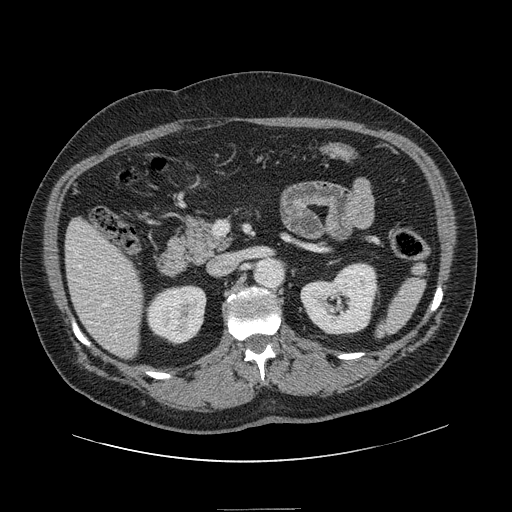
Contrast-enhanced abdominal CT, one axial slice. Position 60 of 154 along the scan axis. 120 kVp. Intravenous contrast given. Soft-tissue window (W 400 / L 40 HU). 2.5 mm slice thickness. 512 × 512 image matrix. Male patient, age 61 years. Case-level facts recorded for this patient, not image findings: diagnosis: colorectal cancer liver metastases, imaged before liver resection; multiple liver metastases: yes; largest metastasis: 2.6 cm; chemotherapy before resection: no.
Structures marked on this image (outlined manually by an expert reader):
- hepatic veins: bounding box <79,265,117,337> (left, top, right, bottom; pixels)
- liver: <67,220,144,358>
- planned liver remnant (the part of the liver to remain after resection): <67,220,144,358>